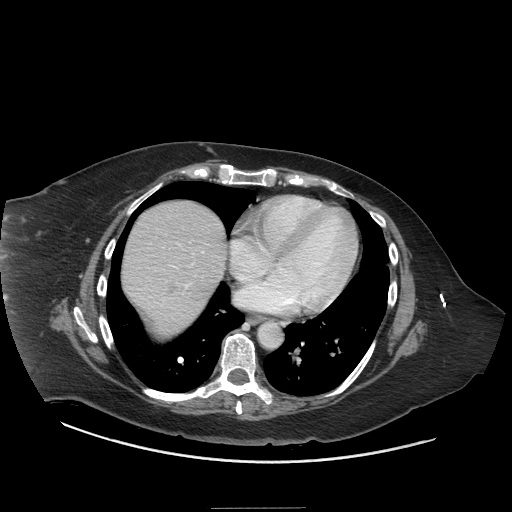
Contrast-enhanced abdominal CT (liver protocol), one axial slice. Slice 69 of 81 in the series (ordered by position). Reconstruction kernel STANDARD. 140 kVp. Soft-tissue window (W 400 / L 40 HU). 2.5 mm slice thickness. 512 × 512 image matrix. From the clinical record (not read from this slice): diagnosis: hepatocellular carcinoma (patient treated with transarterial chemoembolisation; whether this scan precedes or follows treatment is not stated here); TNM stage (as recorded): Stage-II; Child-Pugh class: A; tumour differentiation: moderately differentiated.
Structures marked on this image (semi-automatic segmentation, software-assisted and operator-edited):
- liver parenchyma outside the tumour (the mass and vessels are separate outlines, so this box may not span the whole liver): bounding box (x1, y1, x2, y2) in pixels: (122, 200, 226, 334)
- liver vessels: (130, 242, 204, 309)